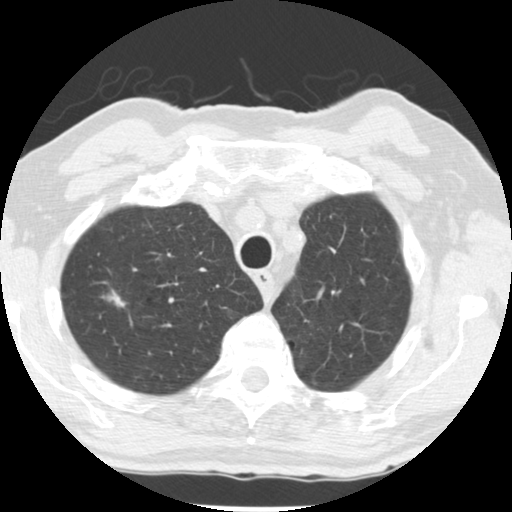
Chest CT (low-dose screening protocol), one axial image; baseline screening round; lung window (W 1500 / L -600 HU). Male, age 69 years at enrolment. Former smoker at enrolment.
- Expert-annotated lung lesion, bounding box <89,271,146,331> (left, top, right, bottom; pixels).
- The screening reader recorded 2 non-calcified nodules or masses ≥4 mm on this exam (right upper lobe, left upper lobe); which of them this box marks is not recorded.
- Official screen result: positive, change unspecified: nodule(s) >= 4 mm or enlarging nodule(s), mass(es), or other non-specific abnormalities suspicious for lung cancer.
- Participant outcome: lung cancer diagnosed 105 days after this screen — adenocarcinoma, NOS, right upper lobe, well differentiated (G1), stage IA (AJCC 6th edition), 17 mm at pathology.